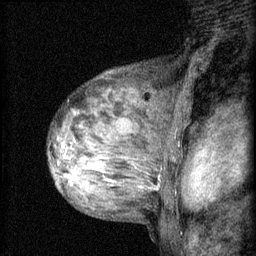
Breast MRI (dynamic contrast-enhanced), one sagittal slice. Slice 43 of 60 in the series (ordered by position). 3 images stored at this slice position (order not interpretable as contrast timing). 1.5 T. TE 4.2 ms, TR 8.2 ms. 256 × 256 image matrix, field of view 180 × 180 mm. Patient: female, 48 years.
Annotated regions visible in this slice (semi-automatic segmentation, software-assisted and operator-edited):
- analysis volume of interest (the breast-tissue region the enhancement analysis was run in; not a lesion): bounding box (x1, y1, x2, y2) in pixels: (54, 138, 133, 191)
- tumour enhancement mask (voxels above the 70 % enhancement threshold inside the analysis volume of interest): (64, 154, 101, 179)